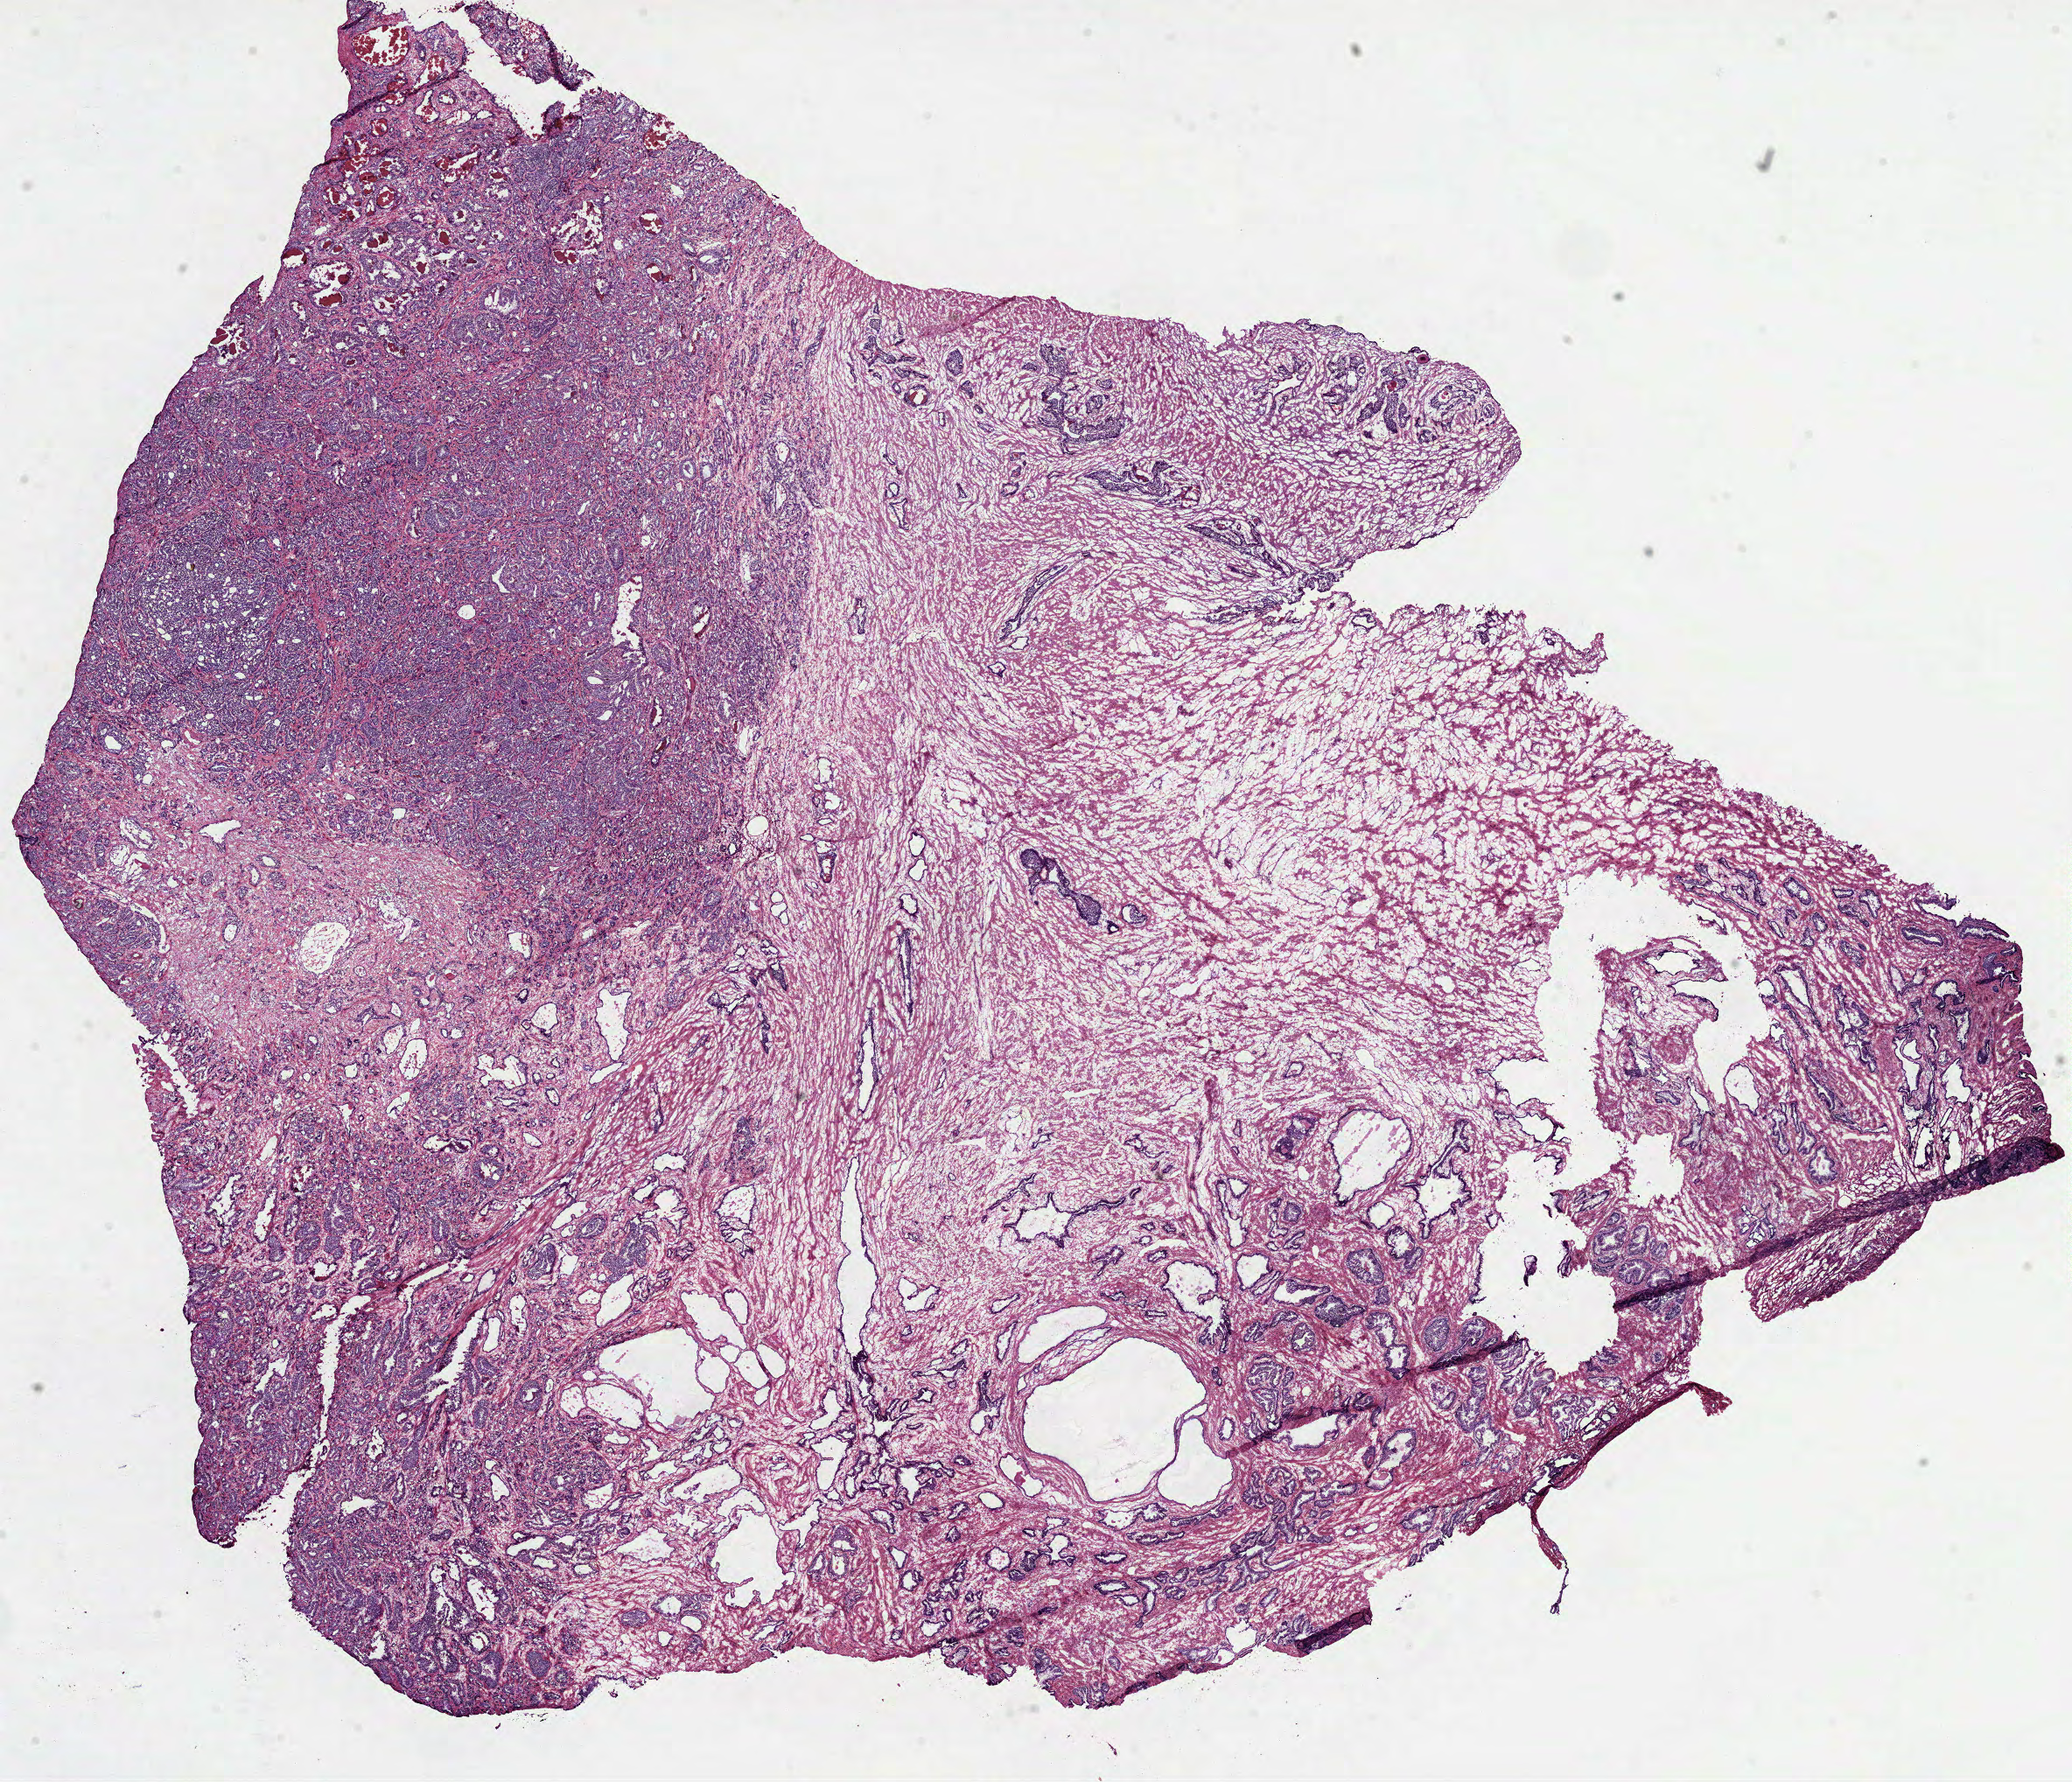
H&E whole-slide image — shown as a low-resolution overview of the whole scanned area (about 19.1 x 16.4 mm). Frozen section from the top of the tissue portion. Primary tumour sample from the prostate. Patient: male, age at initial diagnosis 68 years. Gleason score: 7 (4+3). Composition of this section per pathologist review: tumour cells 65%, tumour nuclei 60%, normal cells 20%, stromal cells 15%, necrosis 0%. Inflammatory infiltration, as recorded: lymphocyte infiltration 2%, monocyte infiltration 0%, neutrophil infiltration 0%.
- histologic diagnosis: Acinar cell carcinoma (prostate gland)
- laterality: bilateral
- lymph nodes positive (case pathology): 0 of 18 examined